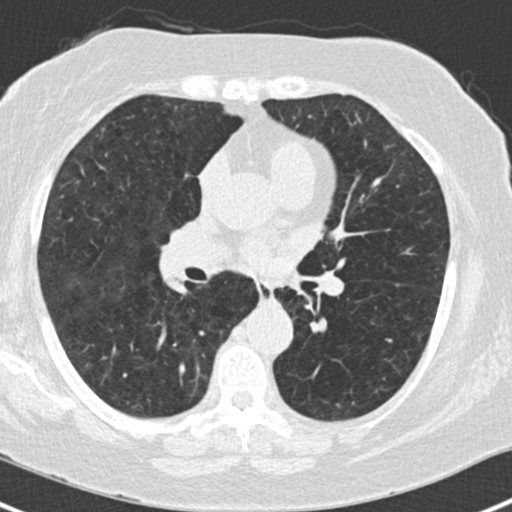
Low-dose screening chest CT, one axial slice. Position 81 of 168 along the scan axis. Reconstruction kernel B30f. 120 kVp. Lung window (W 1500 / L -600 HU). 512 × 512 image matrix, field of view 303 × 303 mm.
Outlined on this slice (expert manual segmentation):
- lesion 1 (tumor, upper lobe of right lung): bounding box [x1, y1, x2, y2] px = [186, 175, 188, 177]